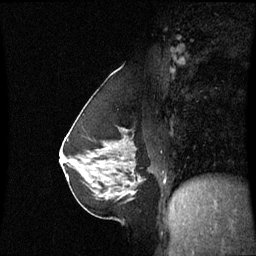
Breast MRI (dynamic contrast-enhanced), one sagittal slice. Slice 31 of 60 in the series (ordered by position). Dynamic contrast-enhanced series, image 2 of 3 at this slice position (ordered by acquisition). 1.5 T. TE 4.2 ms, TR 8.9 ms. 256 × 256 image matrix. Patient: female, 58 years. From the clinical record (not read from this slice): setting: breast cancer imaged before/during neoadjuvant chemotherapy; receptor status: triple-negative.
Annotated regions visible in this slice (semi-automatic segmentation, software-assisted and operator-edited):
- analysis volume of interest (the breast-tissue region the enhancement analysis was run in; not a lesion): bounding box [x1, y1, x2, y2] px = [90, 128, 141, 193]
- tumour enhancement mask (voxels above the 70 % enhancement threshold inside the analysis volume of interest): [130, 184, 135, 193]